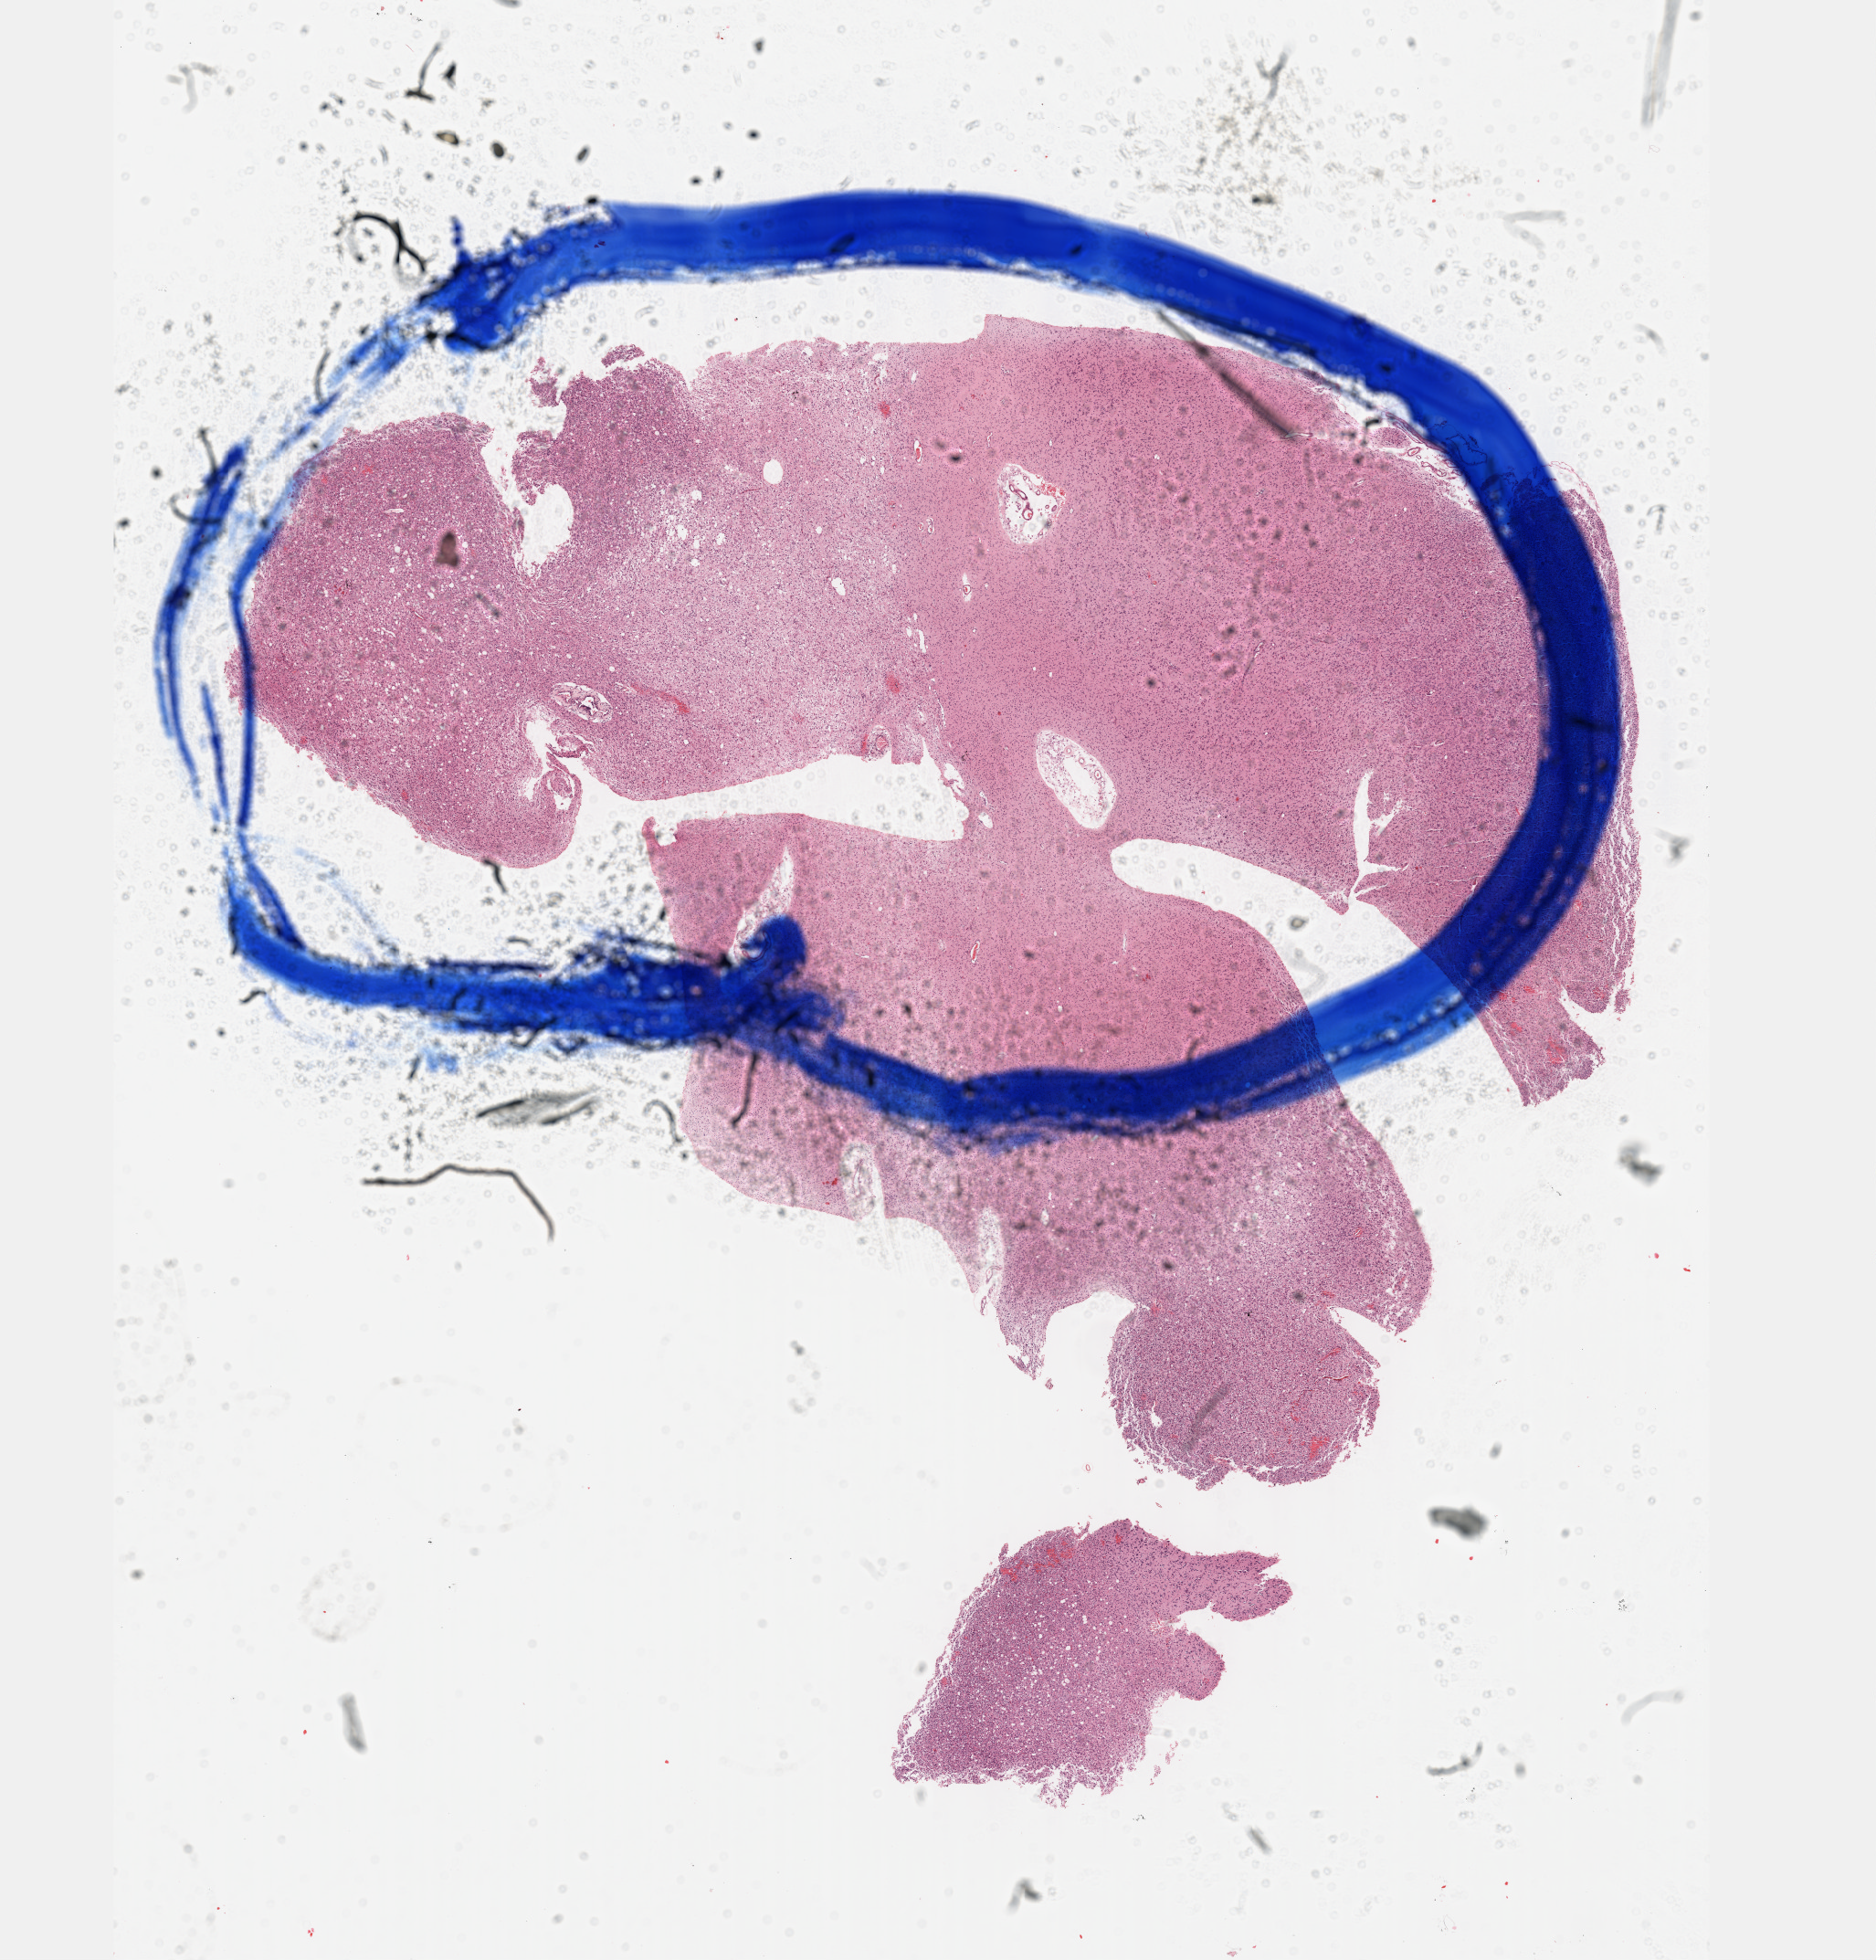
Hematoxylin and eosin (H&E) stained whole-slide image — a low-resolution overview of the entire scanned area, about 16.6 x 17.3 mm; FFPE section; primary tumour sample from the brain. Patient: male, age at initial diagnosis 30 years. Histologic grade: G2 (moderately differentiated).
Laterality: left. Pathologic diagnosis: Mixed glioma.